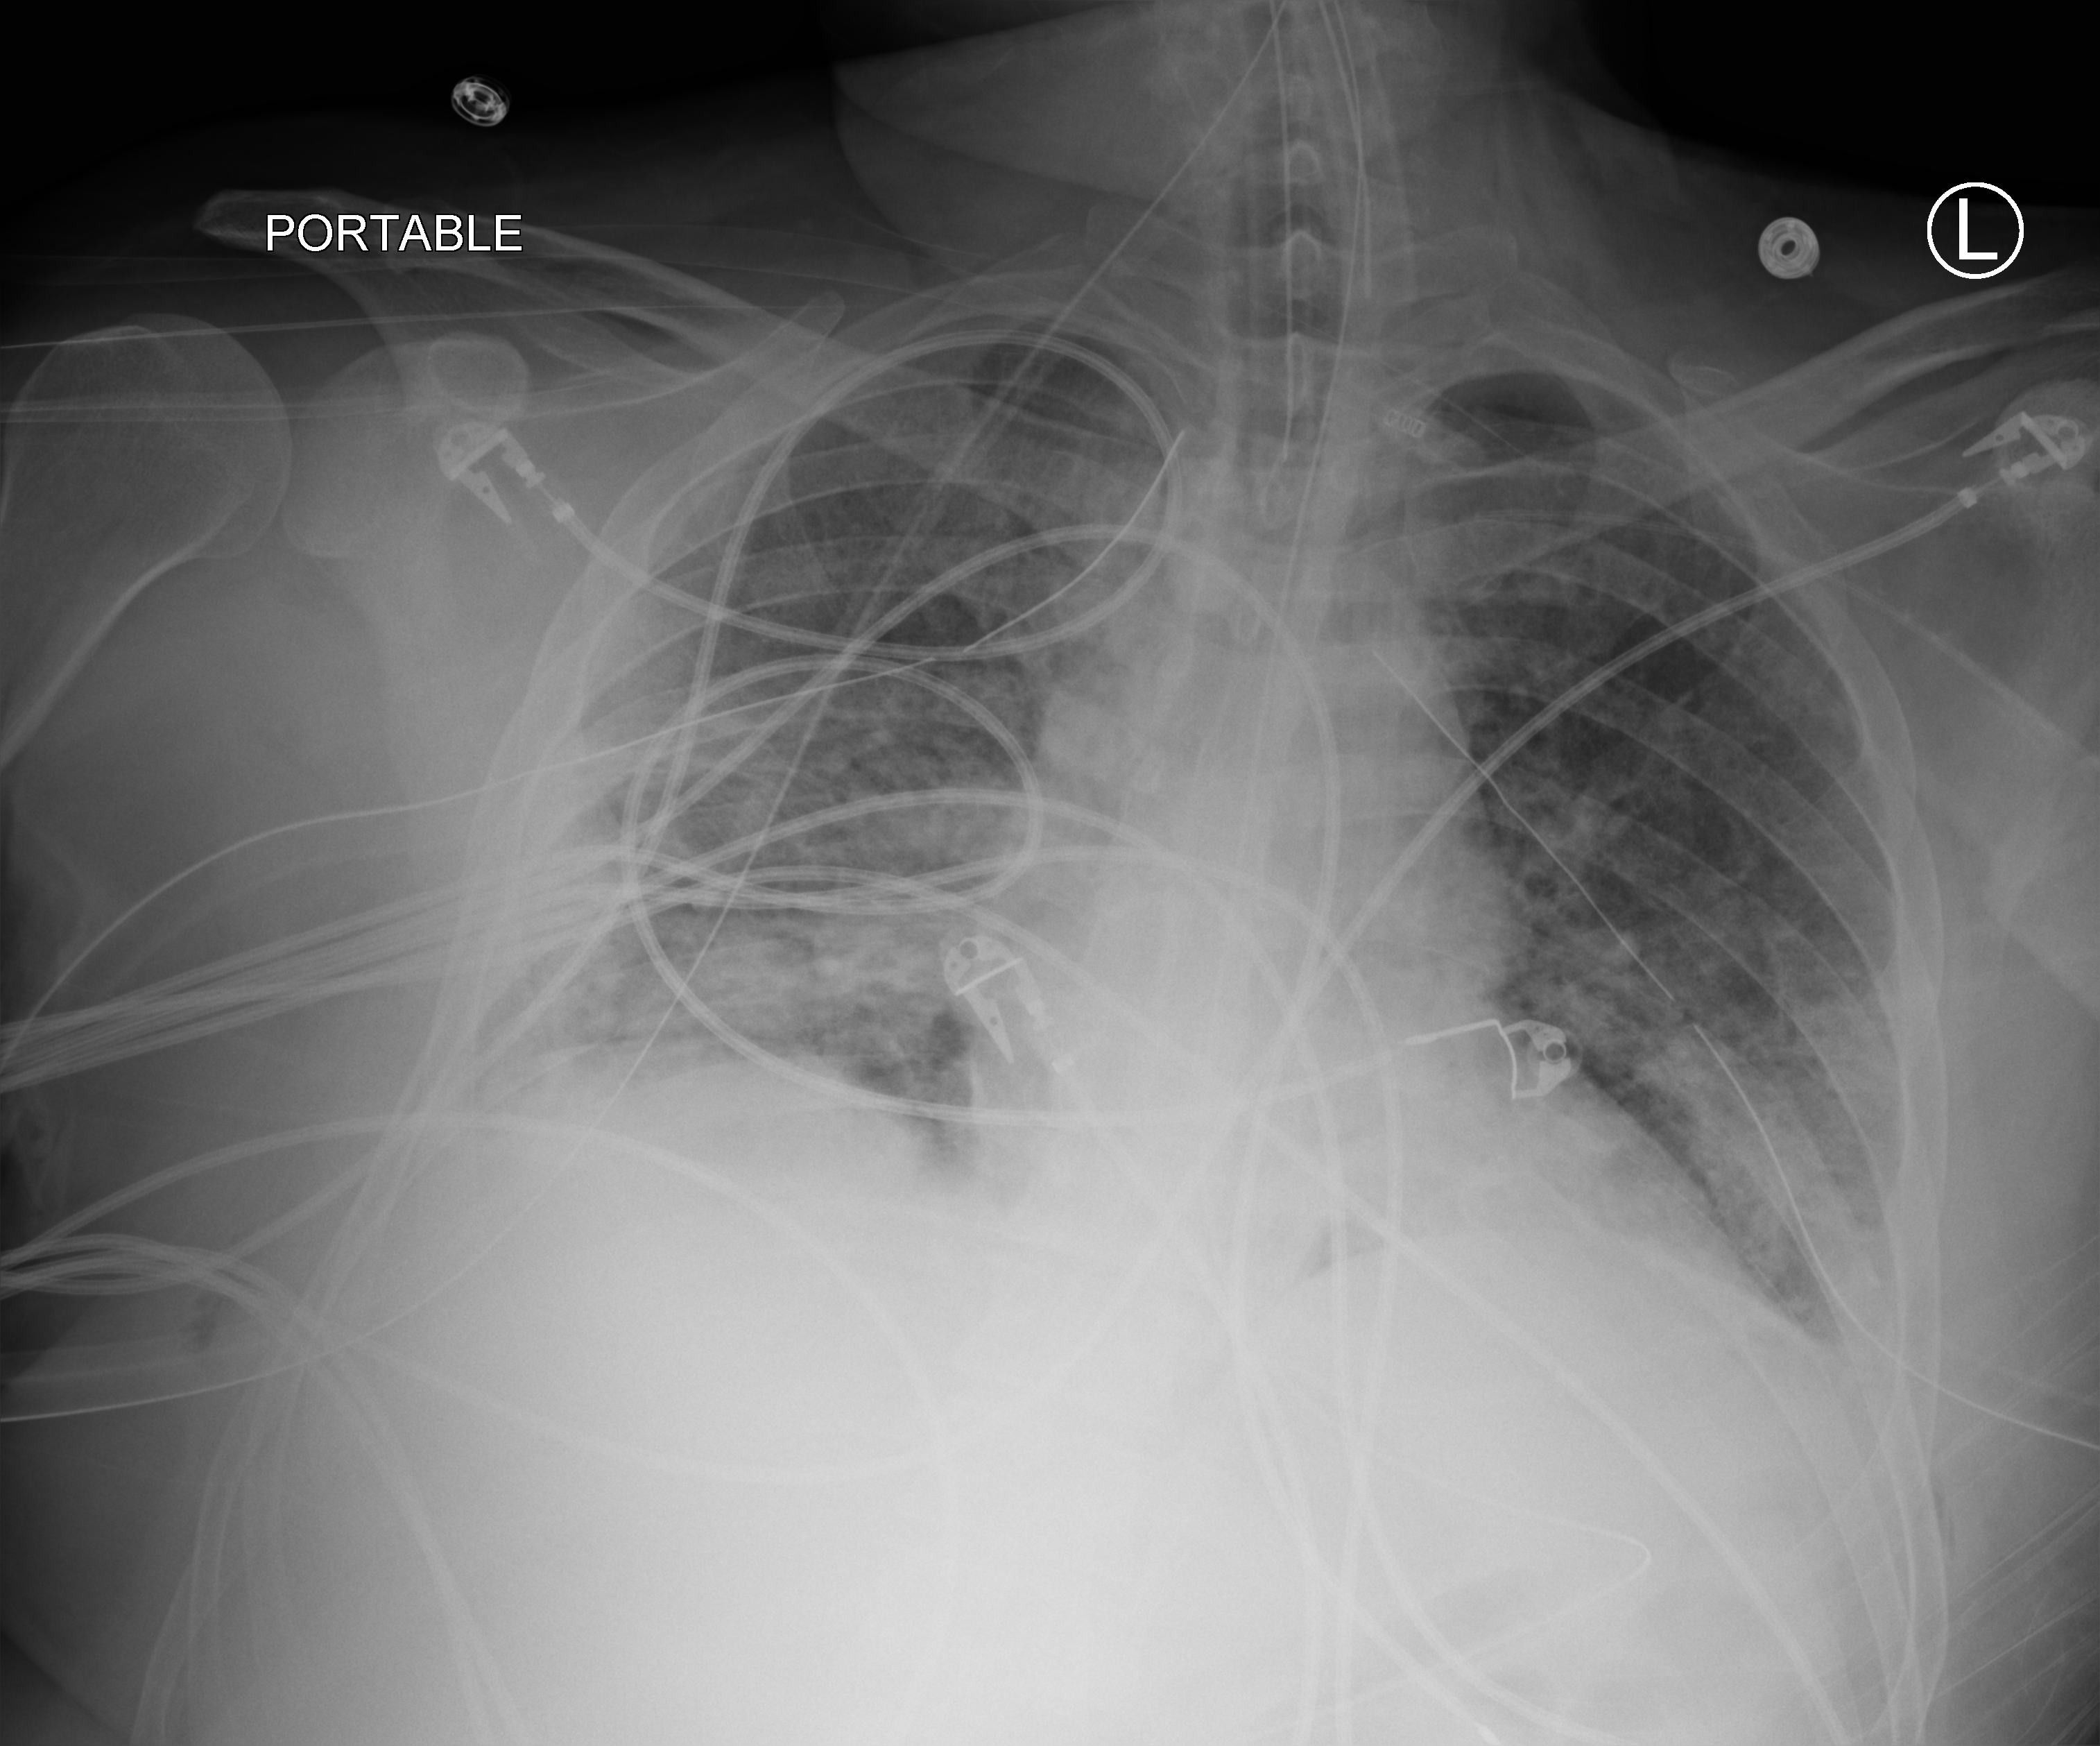
Portable chest radiograph, anteroposterior (AP) projection. Patient hospitalised with COVID-19; male, aged 18–59 years.
From the hospital-stay record, not from the radiograph (when in the stay this image was taken is not recorded): hypertension (admission record): yes; mechanically ventilated during this hospital stay: yes.